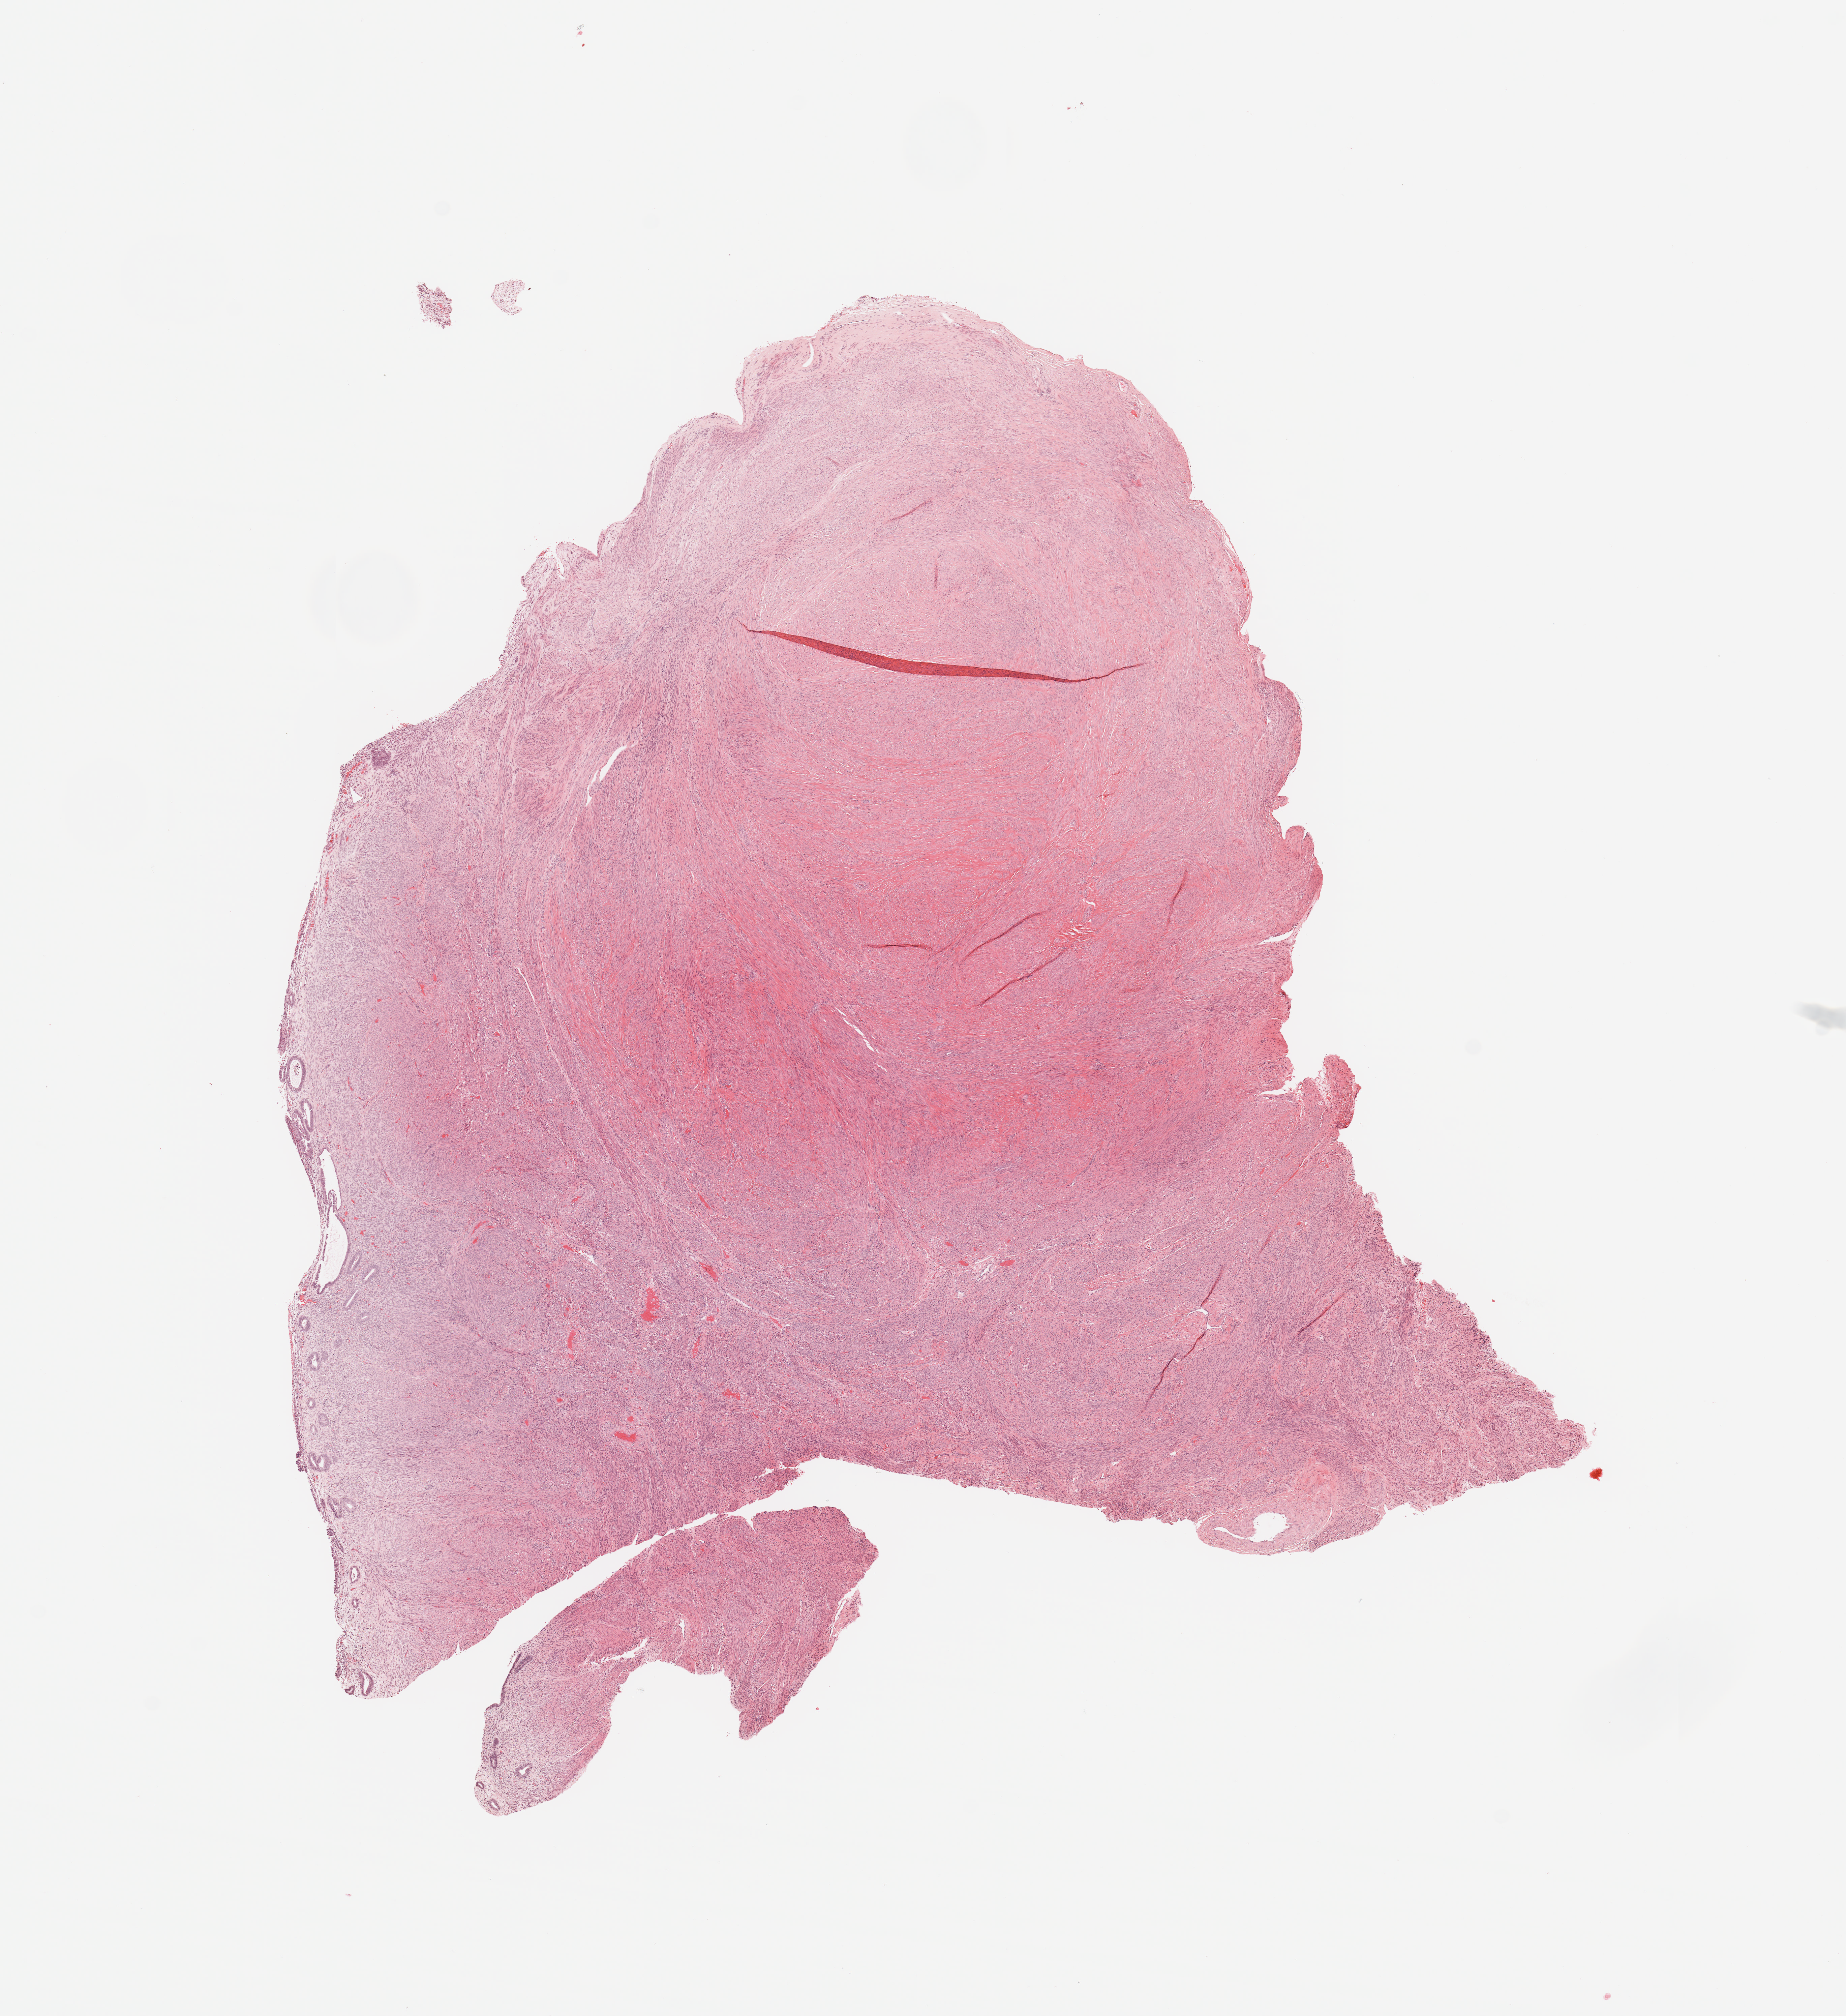
Whole-slide histology image, H&E — a low-resolution overview of the entire scanned area, about 10.8 x 11.8 mm, normal (non-tumour) tissue sample, uterus. 62-year-old female patient.
This section: normal (non-tumour) tissue from the same patient. Patient diagnosis: Endometrioid adenocarcinoma, NOS.